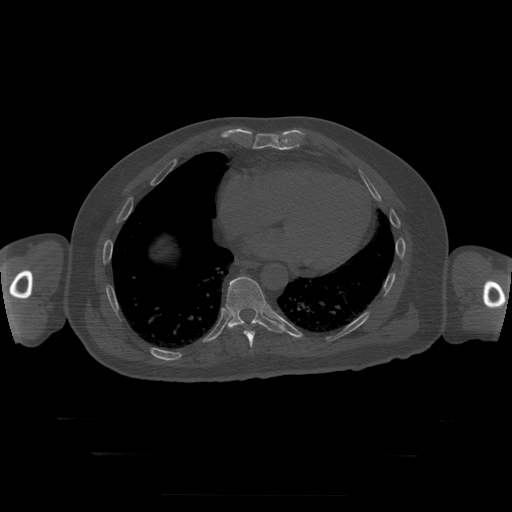
CT including the spine, one axial slice; position 131 of 397 along the scan axis; reconstruction kernel STANDARD; bone window (W 1800 / L 400 HU); 1.25 mm slice thickness; 512 × 512 image matrix. Patient age 73 years. Case-level facts recorded for this patient, not image findings: primary cancer: prostate.
Annotated regions visible in this slice (semi-automatic segmentation, software-assisted and operator-edited):
- T10 vertebra: bounding box [x1, y1, x2, y2] px = [226, 277, 286, 333]
- T9 vertebra: [244, 331, 255, 348]